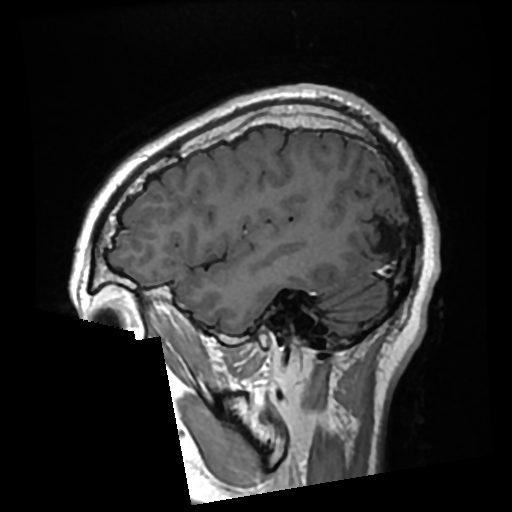
Brain MRI from a brain-tumour surgery series, one sagittal slice. Position 77 of 276 along the scan axis. T1-weighted post-contrast. 512 × 512 image matrix, field of view 250 × 250 mm. Case-level facts recorded for this patient, not image findings: histopathology: Glioma with ependymal features; WHO grade: 2; tumour location: Left Parietal.
Annotated regions visible in this slice (manually delineated by an expert):
- previous resection cavity: bounding box <360,220,397,257> (left, top, right, bottom; pixels)